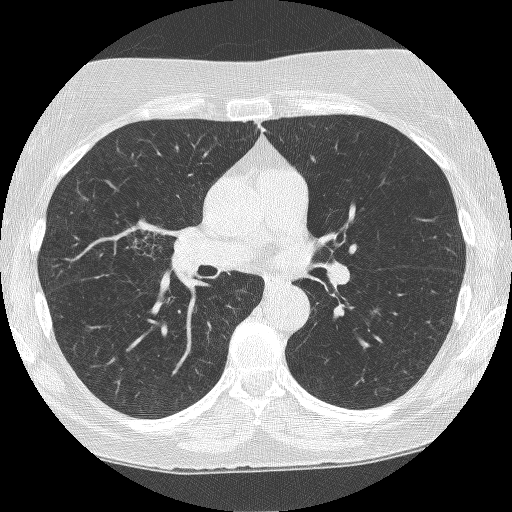
Chest CT (low-dose screening protocol), one axial image, second annual screen, lung window (W 1500 / L -600 HU), 1.25 mm slice thickness, slice 136 of 249 in the series, 512 × 512 image matrix, field of view 308 × 308 mm. Female participant, aged 64 years at enrolment. Former smoker at enrolment.
- Expert reader's lesion annotation, box from (x=117, y=206) to (x=200, y=286) px.
- The screening reader recorded 4 non-calcified nodules or masses ≥4 mm on this exam (right upper lobe, right upper lobe, right upper lobe, left upper lobe); which of them this box marks is not recorded.
- Official screen result: positive, other.